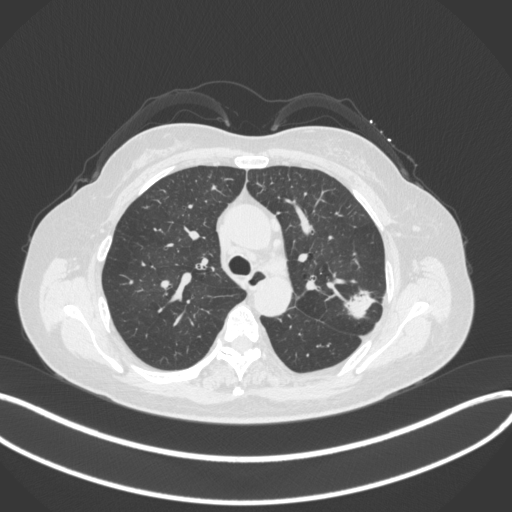
Chest CT, one axial slice; position 235 of 330 along the scan axis; 120 kVp; lung window (W 1500 / L -600 HU); 512 × 512 image matrix. Patient: female, 60 years. Case-level facts recorded for this patient, not image findings: clinical TNM (as recorded): T1c N0 M0.
Annotated regions visible in this slice (rectangle marked by the reading radiologist):
- lung tumour (recorded histology: adenocarcinoma): box from (x=339, y=286) to (x=376, y=319) px